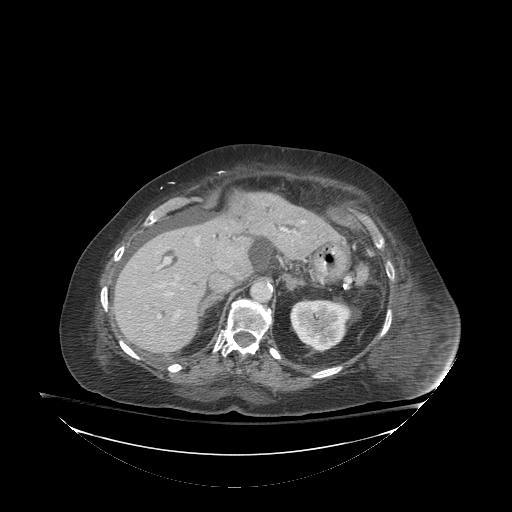
Contrast-enhanced abdominal CT (liver protocol), one axial slice; position 56 of 81 along the scan axis; 140 kVp; soft-tissue window (W 400 / L 40 HU); 2.5 mm slice thickness; 512 × 512 image matrix, field of view 500 × 500 mm. From the clinical record (not read from this slice): diagnosis: hepatocellular carcinoma (patient treated with transarterial chemoembolisation; whether this scan precedes or follows treatment is not stated here); TNM stage (as recorded): Stage-I; Child-Pugh class: B; tumour nodularity: uninodular.
Structures marked on this image (semi-automatically segmented with operator editing):
- liver parenchyma outside the tumour (the mass and vessels are separate outlines, so this box may not span the whole liver): bounding box [x1, y1, x2, y2] px = [114, 192, 330, 354]
- mass: [228, 190, 258, 221]
- liver vessels: [157, 220, 305, 319]